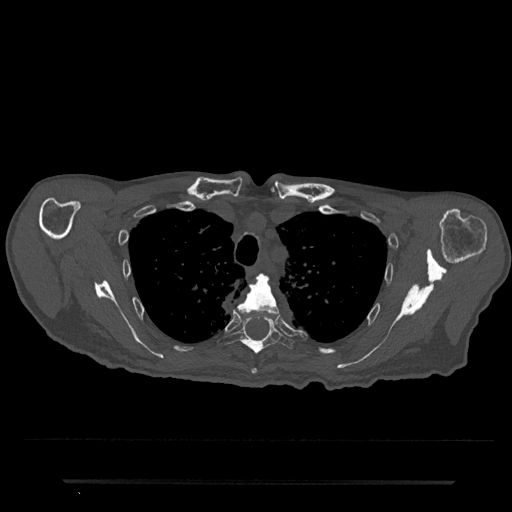
CT including the spine, one axial slice. Reconstruction kernel Br40s/3. 120 kVp. Bone window (W 1800 / L 400 HU). 0.5 mm slice thickness. 512 × 512 image matrix, field of view 427 × 427 mm. Male patient, age 74 years. Case-level facts recorded for this patient, not image findings: primary cancer: prostate.
Outlined on this slice (semi-automatic segmentation, software-assisted and operator-edited):
- T4 vertebra: bounding box <237,275,280,374> (left, top, right, bottom; pixels)
- T5 vertebra: <218,316,294,355>